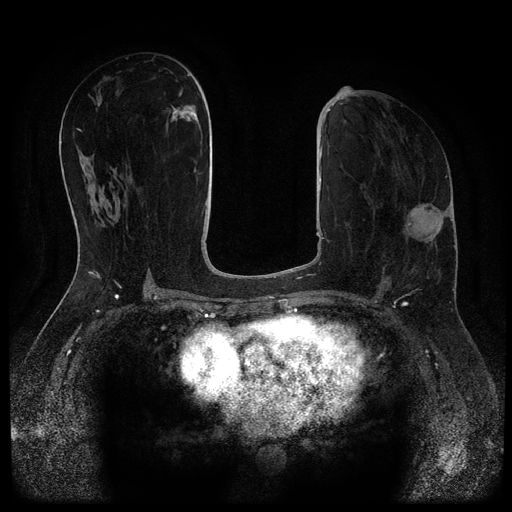
Breast MRI (dynamic contrast-enhanced, multi-phase), one axial slice. Position 49 of 116 along the scan axis. Dynamic contrast-enhanced series, time point 2 of 5 at this slice position (early post-contrast). 1.5 T. TE 2.7 ms, TR 5.4 ms. 2 mm slice thickness. 512 × 512 image matrix, field of view 330 × 330 mm. Patient: female, 58 years.
Structures marked on this image (semi-automatically segmented with operator editing):
- breast lesion (labelled benign in the annotation): box from (x=170, y=106) to (x=200, y=126) px